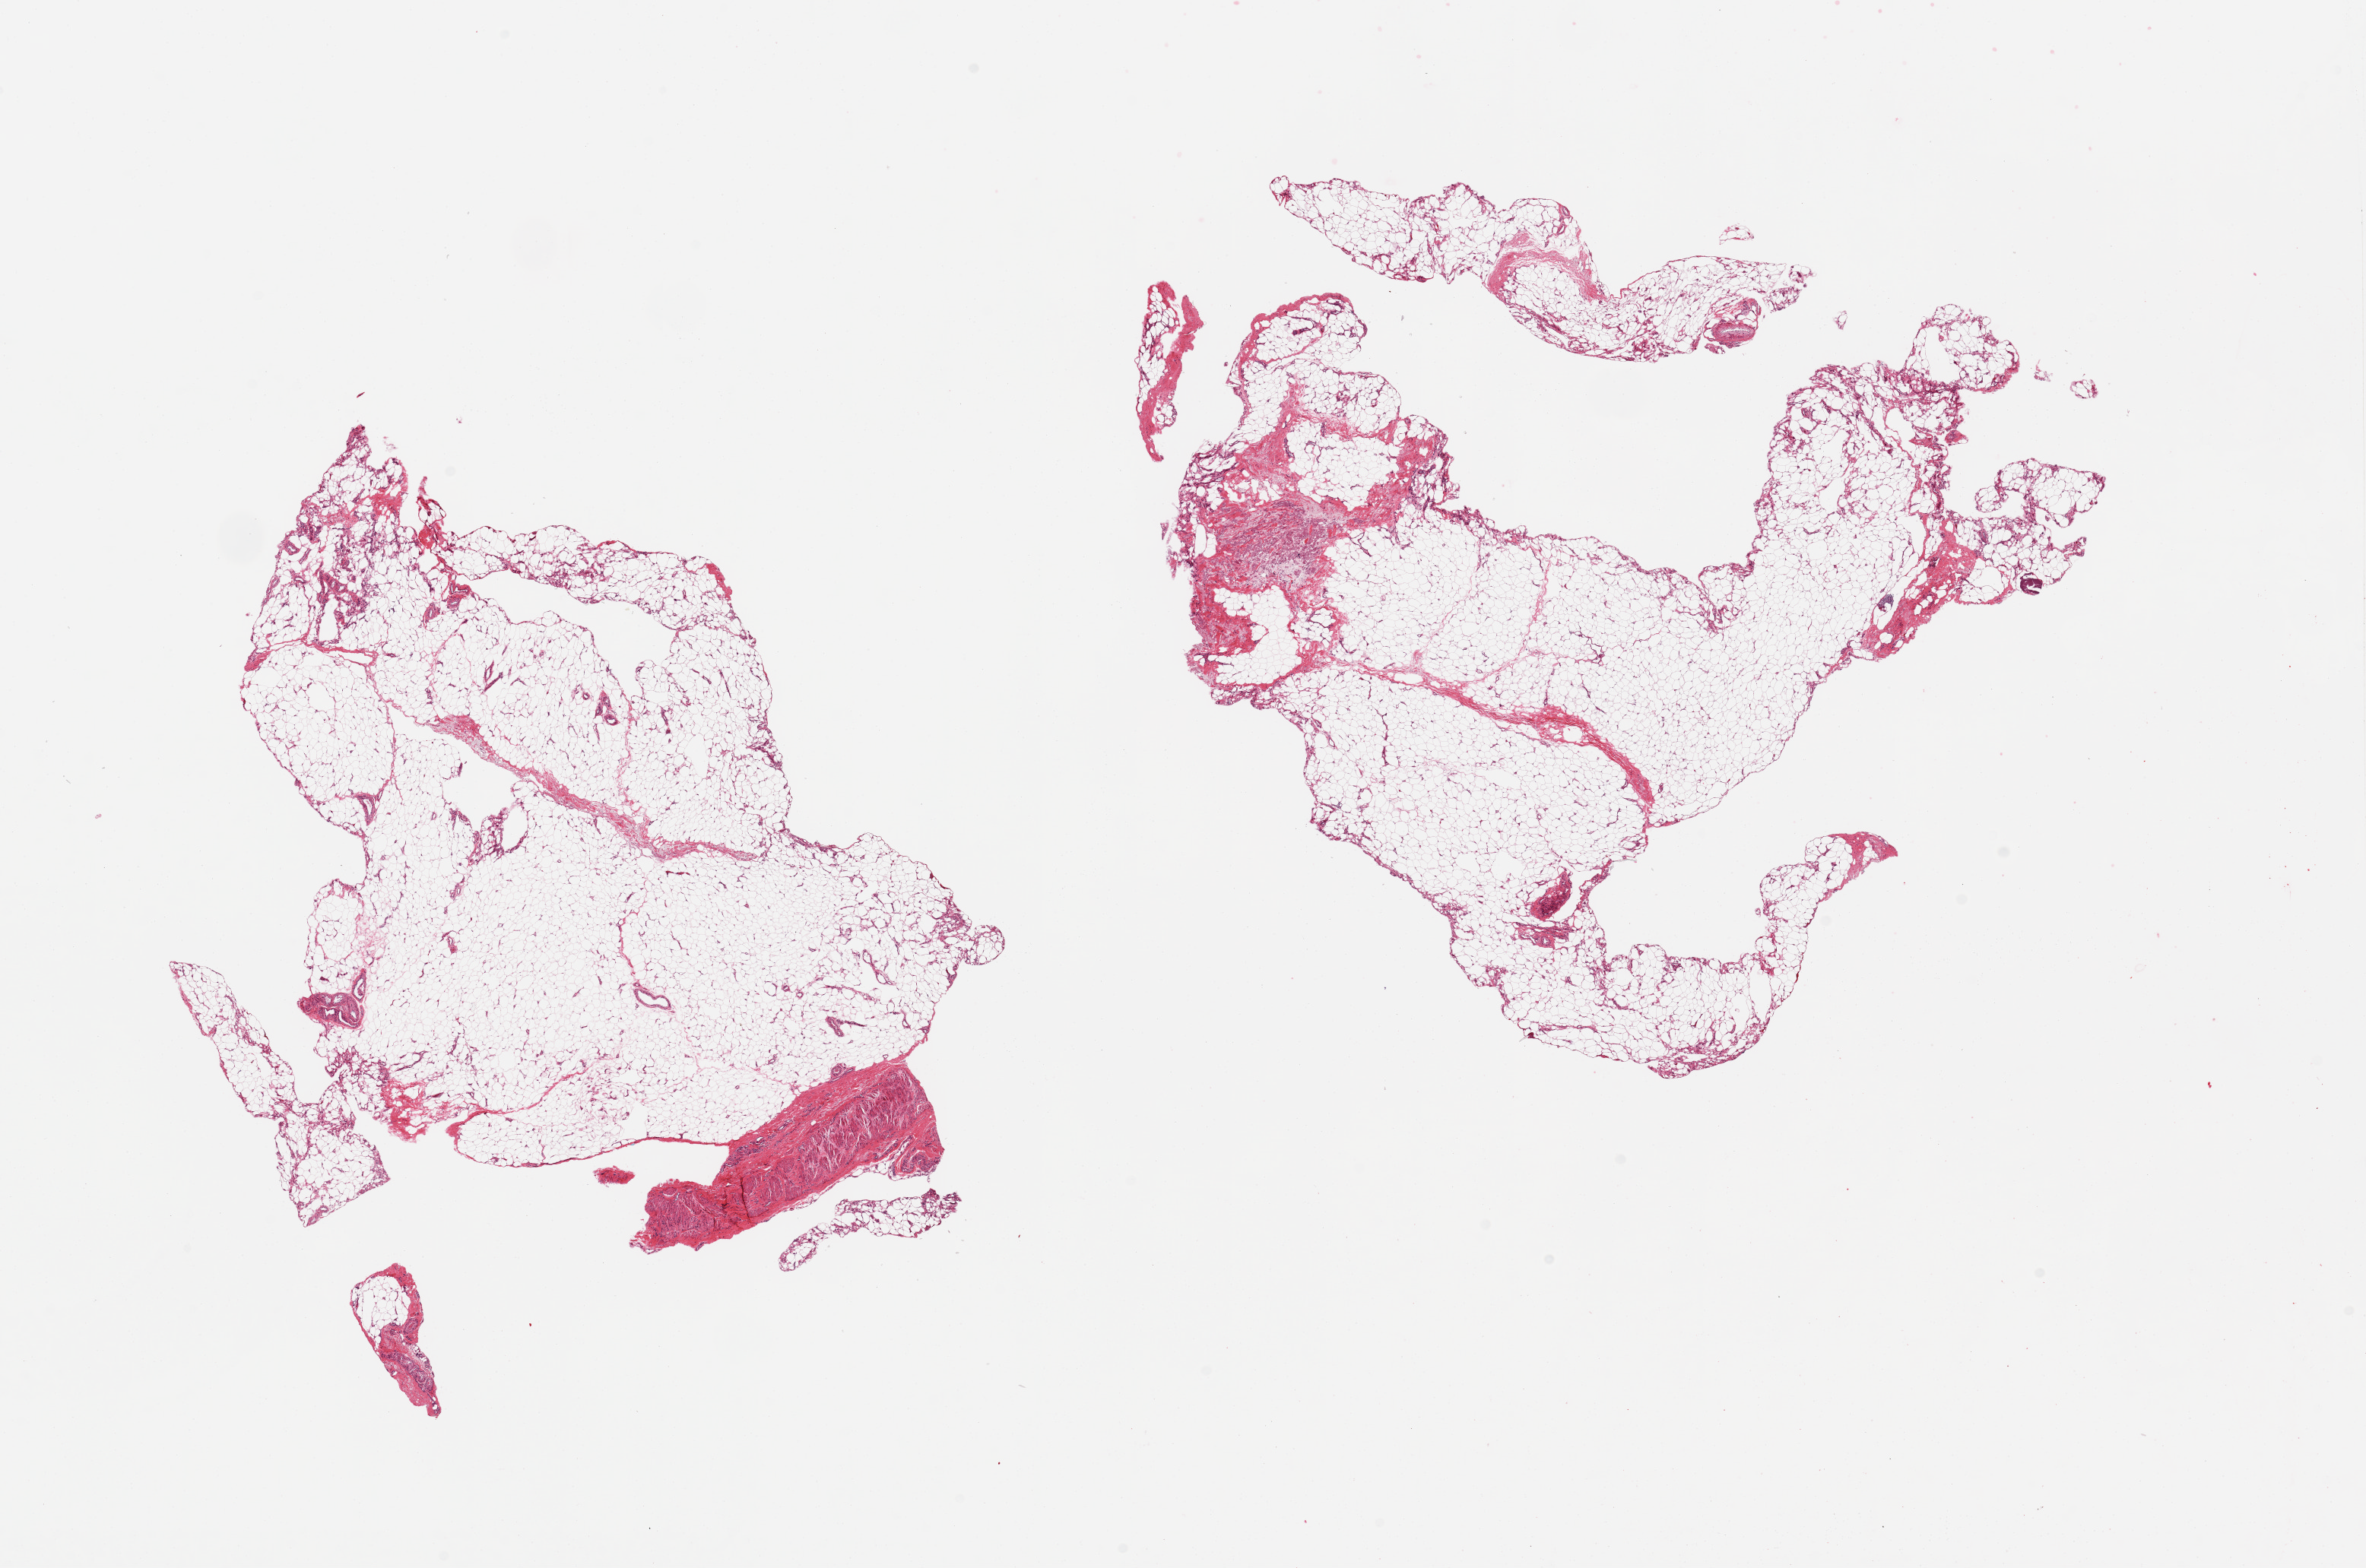
Hematoxylin and eosin (H&E) whole-slide image, low-resolution overview of the scanned area, about 24.6 x 16.3 mm (slide scanned at 20x), PAXgene-fixed paraffin-embedded (PFPE) section, section of adipose tissue (target tissue), tissue donor sample. Donor sex: male.
Review note (as recorded): 2 pieces; fat with some vessels/fibrous tissue (~10%).